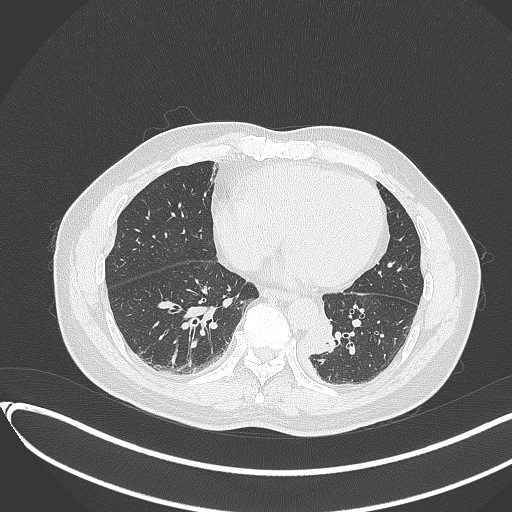
Chest CT, one axial slice; position 115 of 417 along the scan axis; reconstruction kernel B70f; 120 kVp; lung window (W 1500 / L -600 HU); 1 mm slice thickness; 512 × 512 image matrix, field of view 400 × 400 mm. Patient: male, 54 years. From the clinical record (not read from this slice): clinical TNM (as recorded): T3 N0 M0.
Structures marked on this image (rectangle marked by the reading radiologist):
- lung tumour (recorded histology: squamous cell carcinoma): box from (x=301, y=311) to (x=336, y=358) px